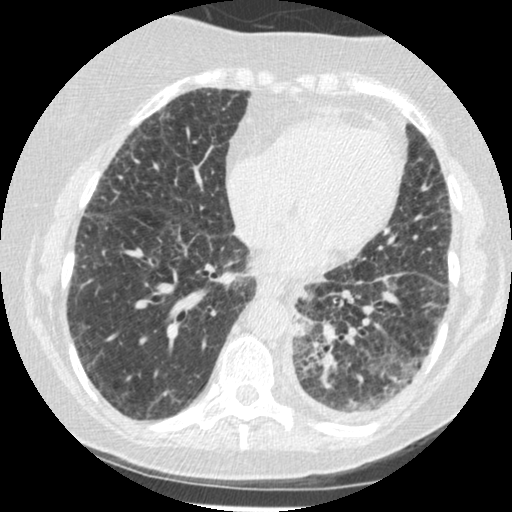
Low-dose screening chest CT, one axial slice. Slice 71 of 341 in the series (ordered by position). Reconstruction kernel STANDARD. 120 kVp. Lung window (W 1500 / L -600 HU). 1.25 mm slice thickness. 512 × 512 image matrix, field of view 310 × 310 mm.
Outlined on this slice (expert manual segmentation):
- lesion 1 (tumor, lower lobe of left lung): box from (x=294, y=326) to (x=306, y=334) px